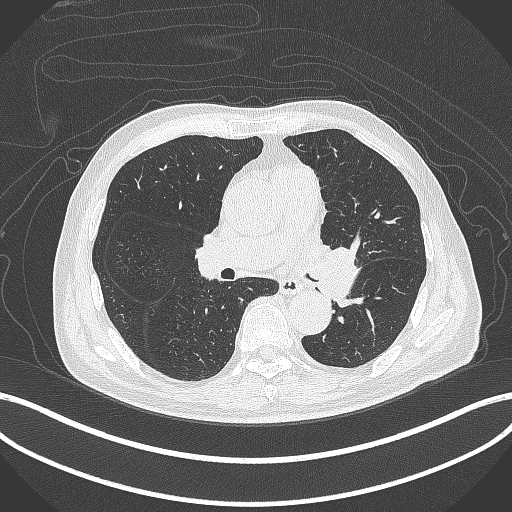
Chest CT, one axial slice; position 235 of 417 along the scan axis; lung window (W 1500 / L -600 HU); 1 mm slice thickness; 512 × 512 image matrix, field of view 400 × 400 mm. Patient: male, 77 years. Case-level facts recorded for this patient, not image findings: clinical TNM (as recorded): T3 N1 M0.
Structures marked on this image (rectangle marked by the reading radiologist):
- lung tumour (recorded histology: adenocarcinoma): bounding box <304,237,367,307> (left, top, right, bottom; pixels)